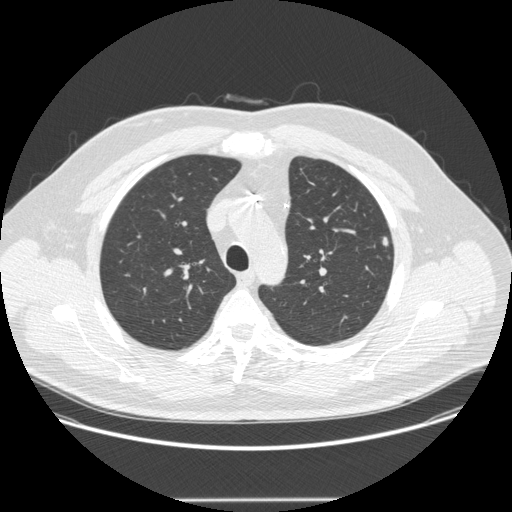
Axial slice from a low-dose chest CT screening exam. Baseline screening round. Lung window (W 1500 / L -600 HU). Male participant, aged 55 years at enrolment.
Lesion marked by an expert reader, box from (x=373, y=232) to (x=402, y=261) px. The exam's reader record, not a measurement of the box and not confirmed to be the same lesion: non-calcified nodule or mass ≥4 mm, left upper lobe, 5 × 4 mm, smooth margins, soft tissue attenuation. Official screen result: positive, change unspecified: nodule(s) >= 4 mm or enlarging nodule(s), mass(es), or other non-specific abnormalities suspicious for lung cancer. Participant outcome: lung cancer diagnosed 462 days after this screen (after the second annual screen) — adenocarcinoma, NOS, left upper lobe, moderately differentiated (G2), stage IA (AJCC 6th edition), 9 mm at pathology.